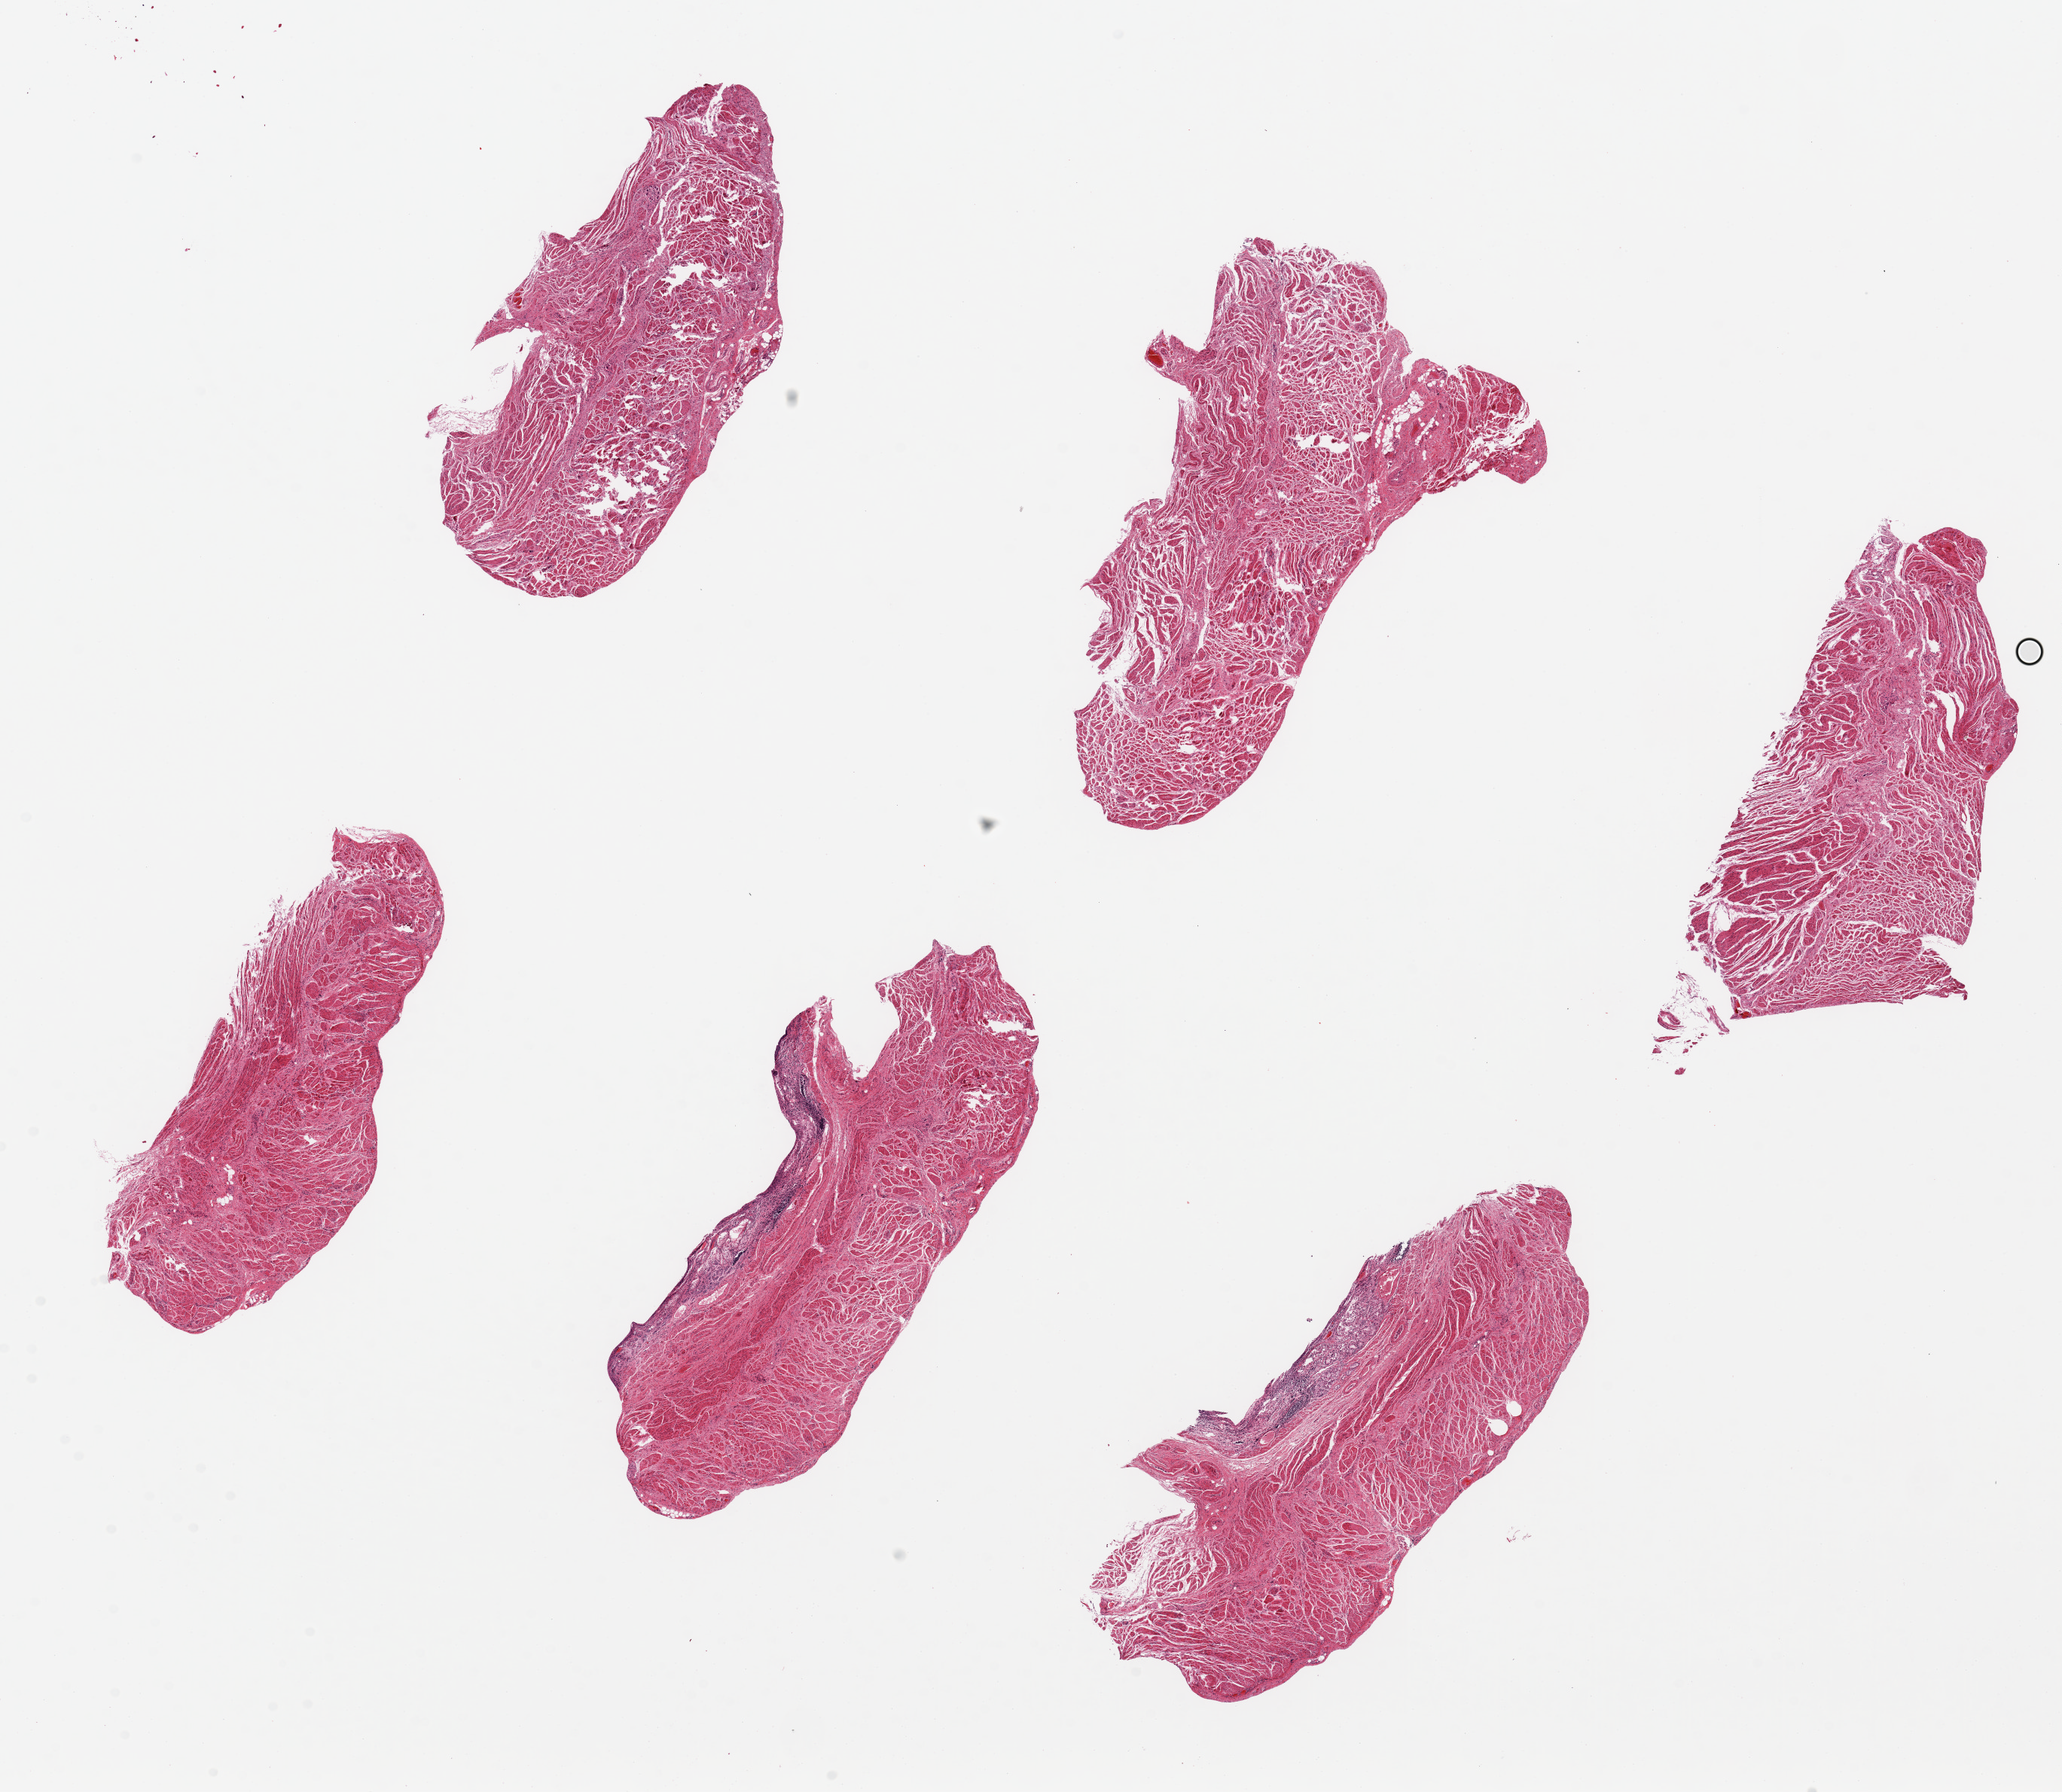
H&E whole-slide image, a low-resolution overview of the entire scanned area, about 21.7 x 18.8 mm; PAXgene-fixed, paraffin-embedded tissue; target tissue: gastroesophageal junction; tissue donor sample. Donor sex: male.
• reviewer comment on this tissue sample: 6 pieces, up to 7x3mm